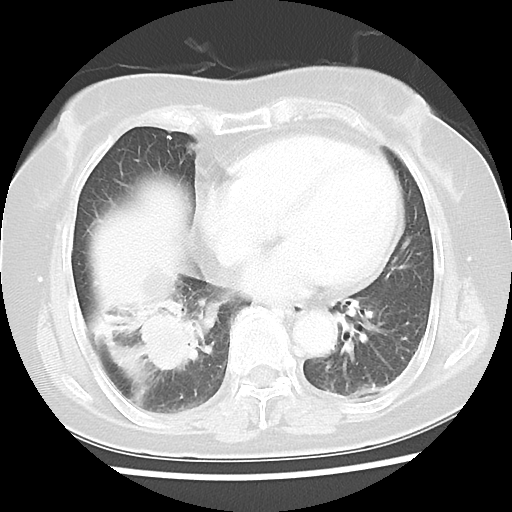
Chest CT, one axial slice; position 16 of 45 along the scan axis; reconstruction kernel LUNG; 120 kVp; lung window (W 1500 / L -600 HU); 5 mm slice thickness; 512 × 512 image matrix, field of view 312 × 312 mm. Patient: female, 65 years. Case-level facts recorded for this patient, not image findings: clinical TNM (as recorded): T2 N3 M0.
Structures marked on this image (bounding box drawn by a radiologist):
- lung tumour (recorded histology: adenocarcinoma): box from (x=136, y=311) to (x=202, y=375) px